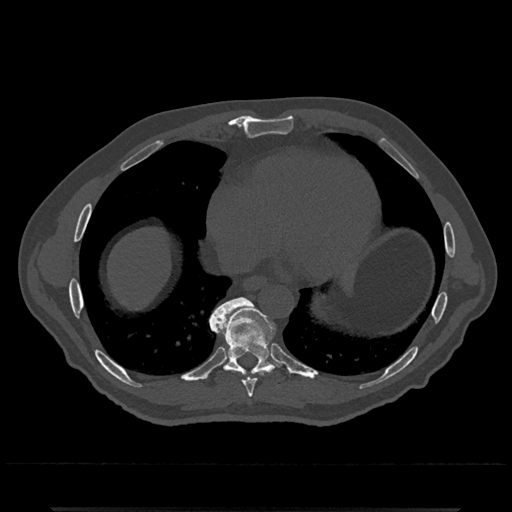
CT including the spine, one axial slice. Slice 637 of 797 in the series (ordered by position). Reconstruction kernel Br40s/3. 120 kVp. Bone window (W 1800 / L 400 HU). 512 × 512 image matrix, field of view 393 × 393 mm. Patient: male, 67 years. Case-level facts recorded for this patient, not image findings: primary cancer: prostate.
Structures marked on this image (semi-automatic segmentation, software-assisted and operator-edited):
- T8 vertebra: box from (x=243, y=374) to (x=256, y=398) px
- T9 vertebra: (x=210, y=297)–(x=278, y=375)